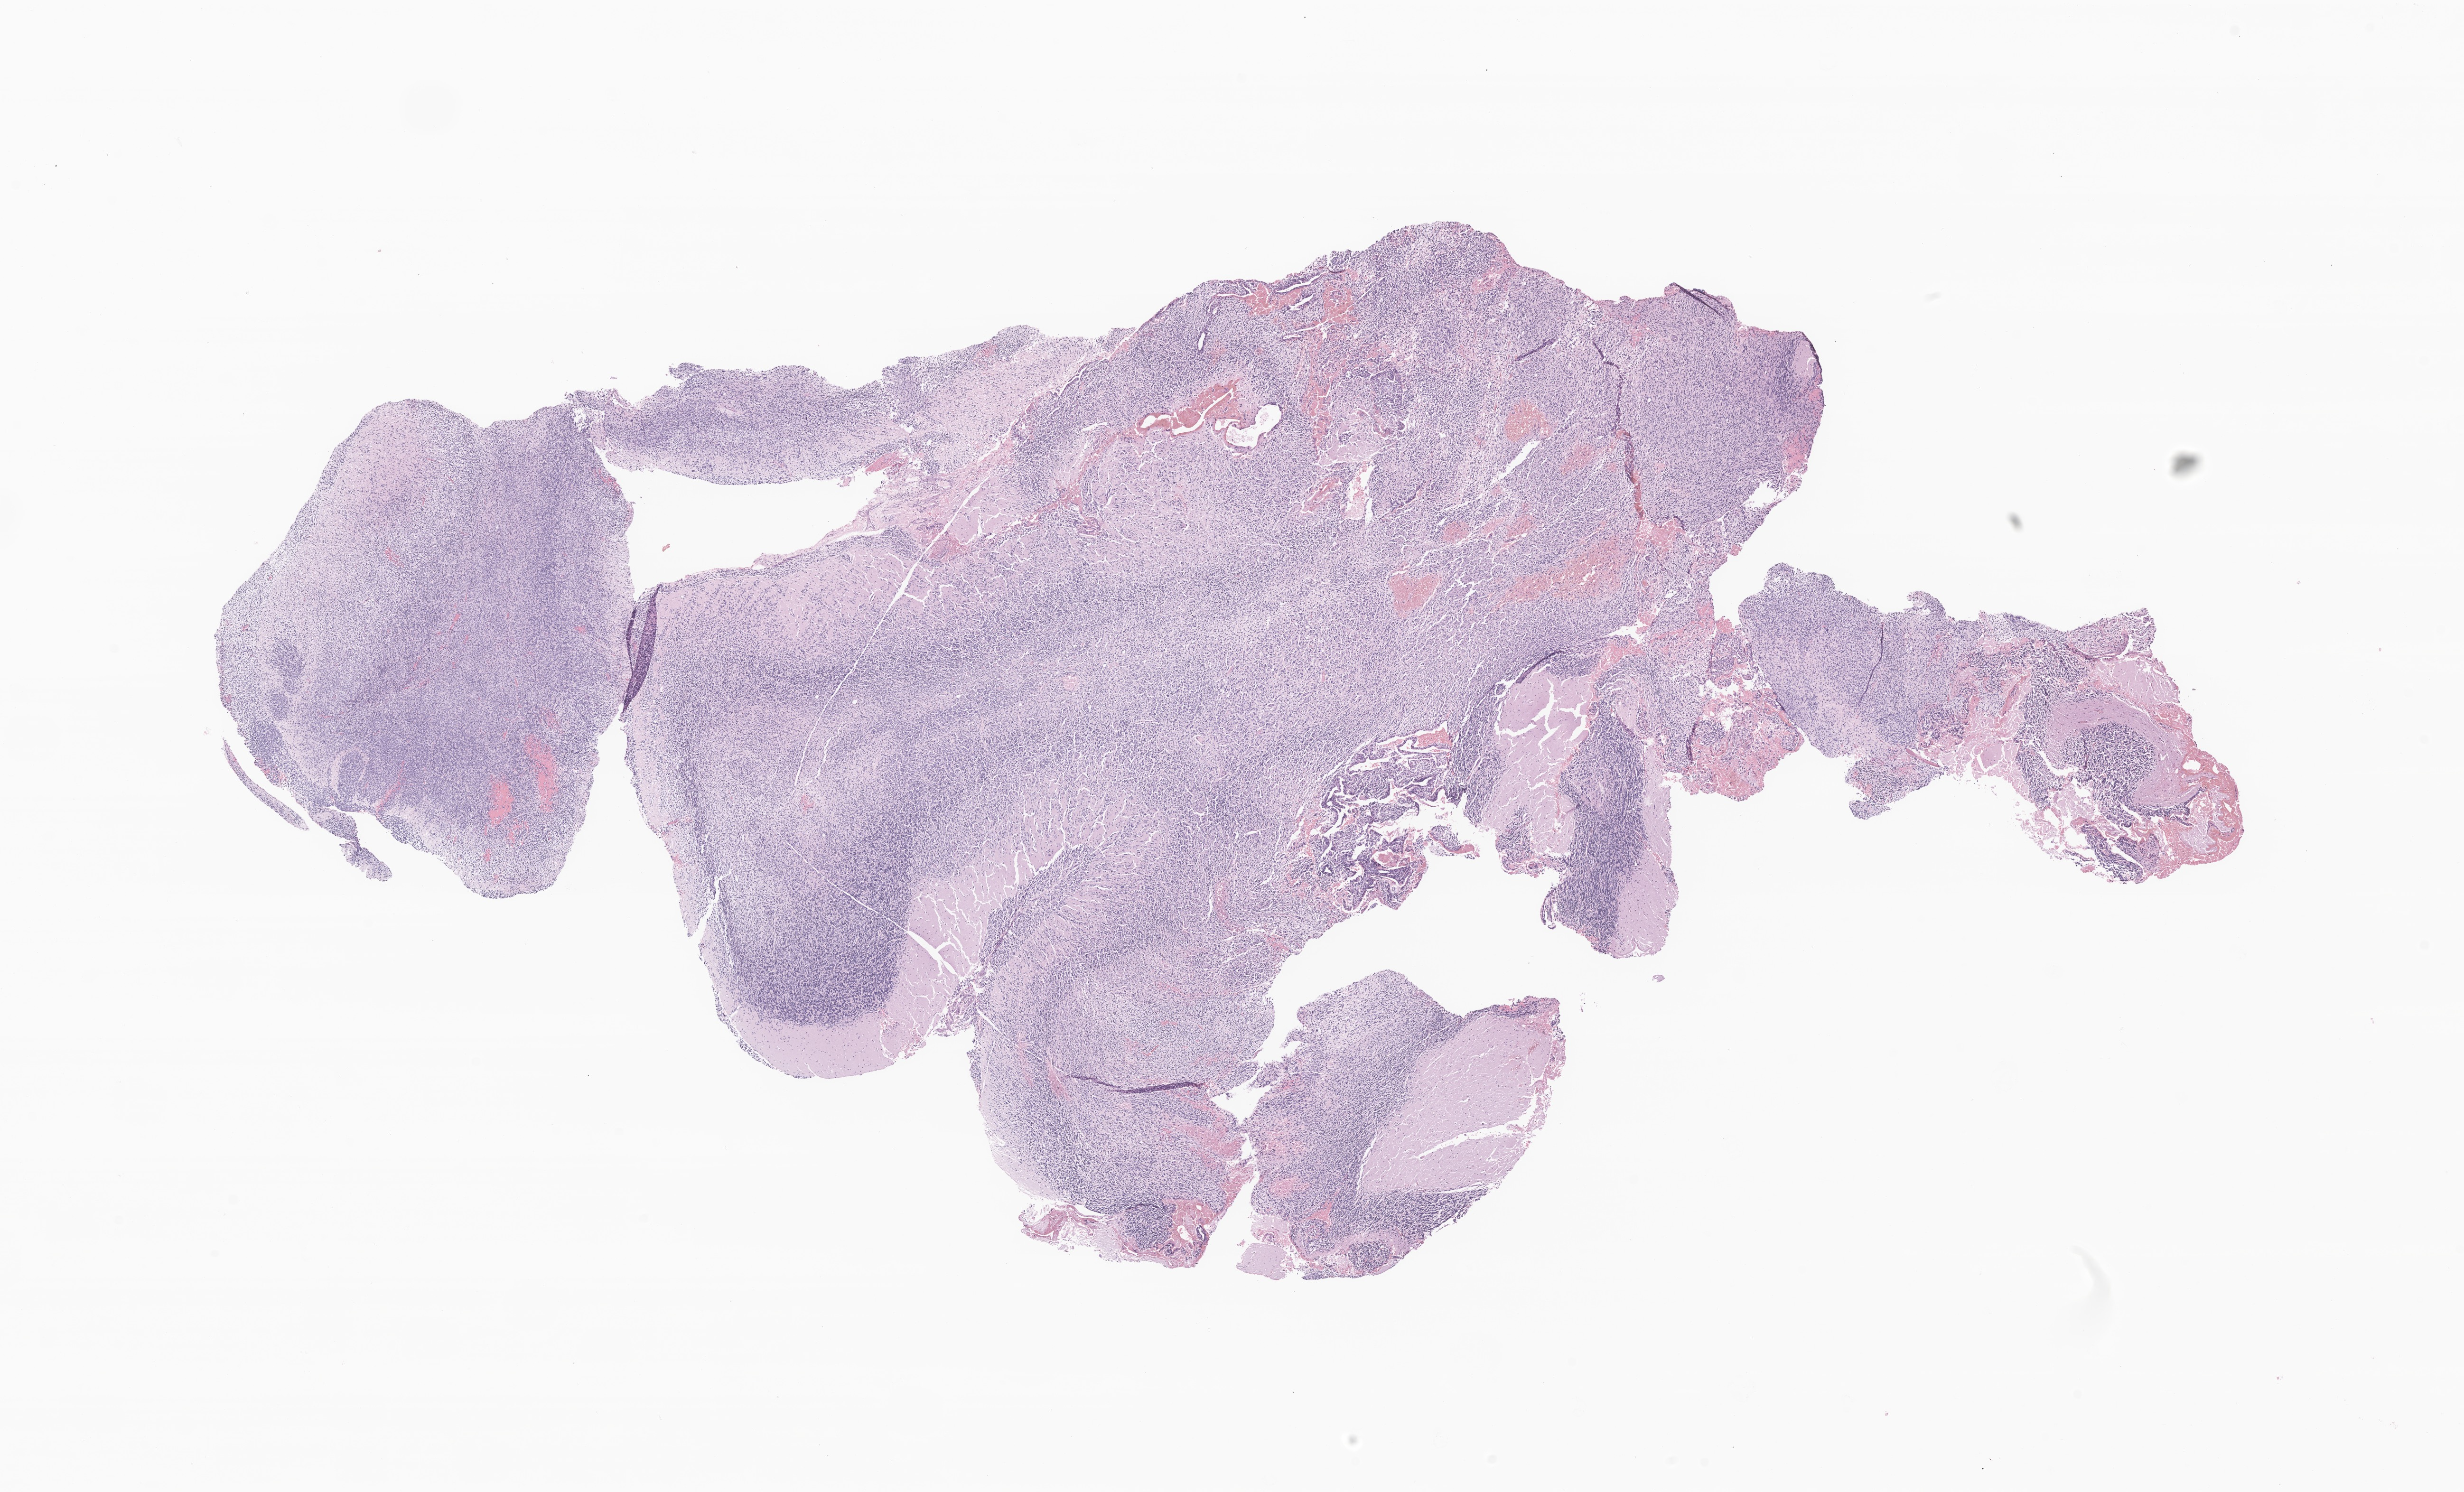
Digitized hematoxylin and eosin (H&E)-stained section of tumor tissue from the brain, whole scanned area (about 21.9 x 13.3 mm) shown as a low-resolution overview, formalin-fixed, paraffin-embedded (FFPE) tissue. Patient male; age 181 months.
- diagnosis: Medulloblastoma, NOS